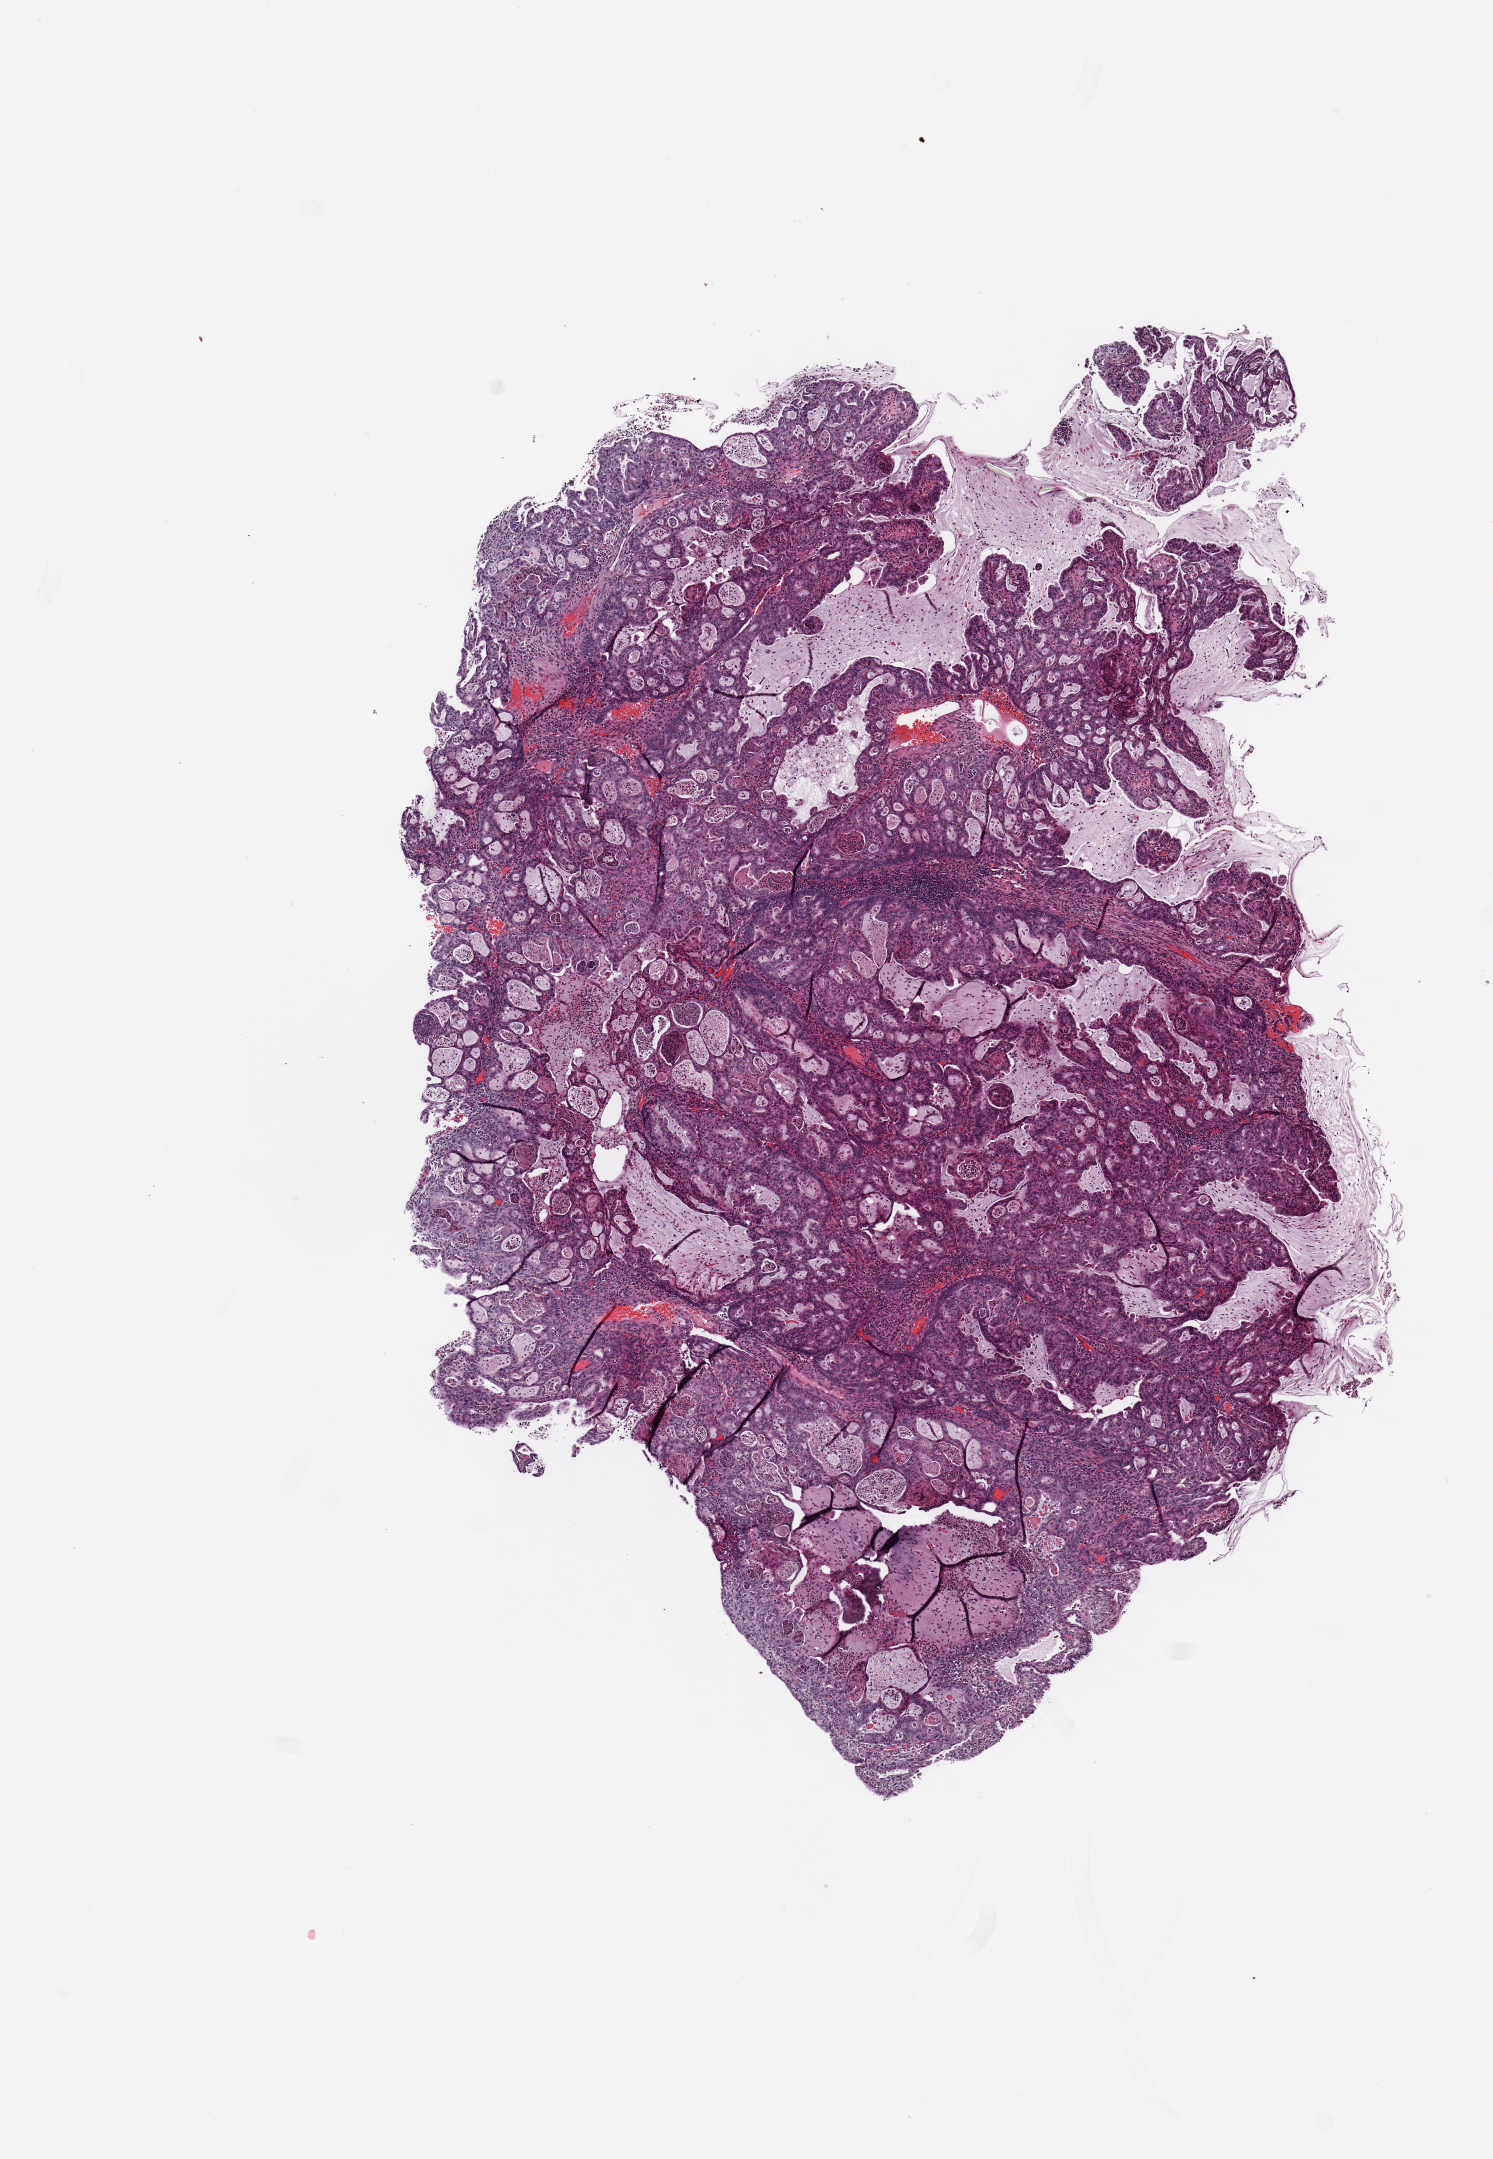
Whole-slide histology image, H&E — shown as a low-resolution overview of the whole scanned area (about 5.9 x 8.5 mm, acquisition: 20x scan). Tumour tissue sample, sampled site: uterus. Female, 69 y/o. Histologic grade: G2 (moderately differentiated). Slide review estimates, as recorded: tumour nuclei 80%, necrosis 0%.
Diagnosis: Endometrioid adenocarcinoma, NOS. AJCC pathologic stage: IA.